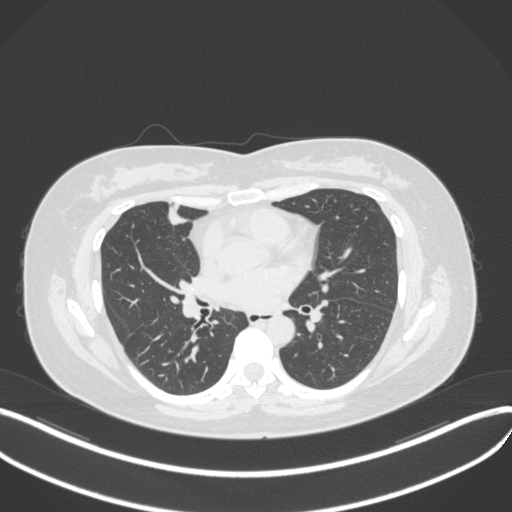
Chest CT, one axial slice; slice 160 of 272 in the series (ordered by position); lung window (W 1500 / L -600 HU); 1 mm slice thickness; 512 × 512 image matrix, field of view 400 × 400 mm. Patient: female, 42 years. Case-level facts recorded for this patient, not image findings: clinical TNM (as recorded): T1b N0 M0.
Structures marked on this image (rectangle marked by the reading radiologist):
- lung tumour (recorded histology: adenocarcinoma): box from (x=159, y=196) to (x=192, y=226) px